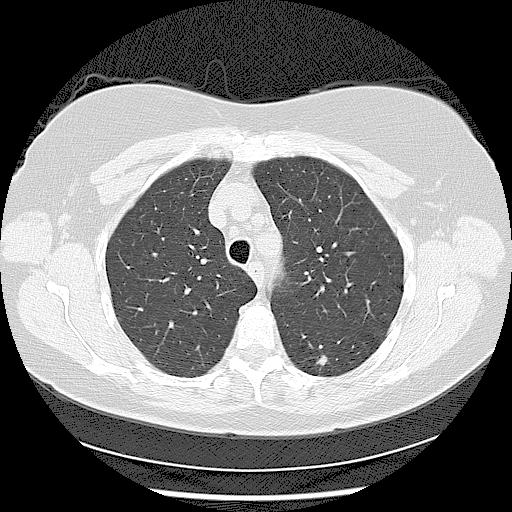
Chest CT (low-dose screening protocol), one axial image. Baseline screening round. Lung window (W 1500 / L -600 HU). Lung (sharp) reconstruction kernel (LUNG). Slice 28 of 116 in the series. 512 × 512 image matrix. Female, age 56 years at enrolment. Current smoker at enrolment.
Lesion marked by an expert reader, box from (x=293, y=337) to (x=343, y=391) px. The screening reader recorded 2 non-calcified nodules or masses ≥4 mm on this exam (left lower lobe, left lower lobe); which of them this box marks is not recorded. Later outcome: lung cancer diagnosed 638 days after this screen (after the second annual screen) — adenocarcinoma, NOS, left lower lobe, moderately differentiated (G2), stage IIA (AJCC 6th edition), 15 mm at pathology.